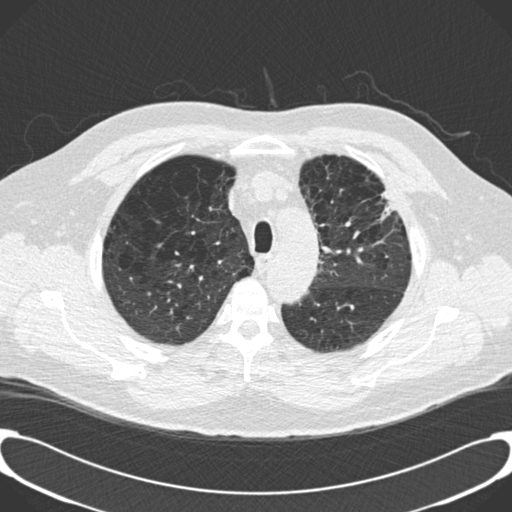
Axial slice from a low-dose chest CT screening exam. Third annual screen. Lung window (W 1500 / L -600 HU). 512 × 512 image matrix, field of view 380 × 380 mm. Male participant, aged 59 years at enrolment. Current smoker at enrolment.
- Expert reader's lesion annotation, box from (x=363, y=176) to (x=409, y=229) px.
- No non-calcified nodule or mass ≥4 mm was recorded by the screening reader at this exam.
- Official screen result: positive, other.
- Lung cancer was diagnosed 134 days after this screen: bronchiolo-alveolar carcinoma, mixed mucinous and non-mucinous, left upper lobe, stage IA (AJCC 6th edition), 20 mm at pathology.